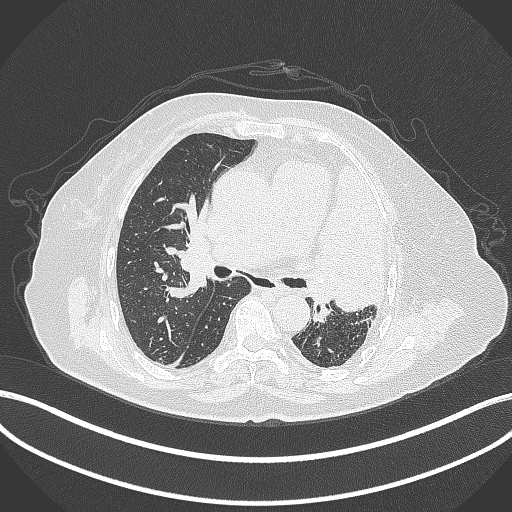
Chest CT, one axial slice. Slice 225 of 399 in the series (ordered by position). 120 kVp. Lung window (W 1500 / L -600 HU). 1 mm slice thickness. 512 × 512 image matrix. Female patient, age 75 years. From the clinical record (not read from this slice): clinical TNM (as recorded): T3 N3 M1.
Outlined on this slice (rectangle marked by the reading radiologist):
- lung tumour (recorded histology: adenocarcinoma): bounding box [x1, y1, x2, y2] px = [308, 160, 394, 315]